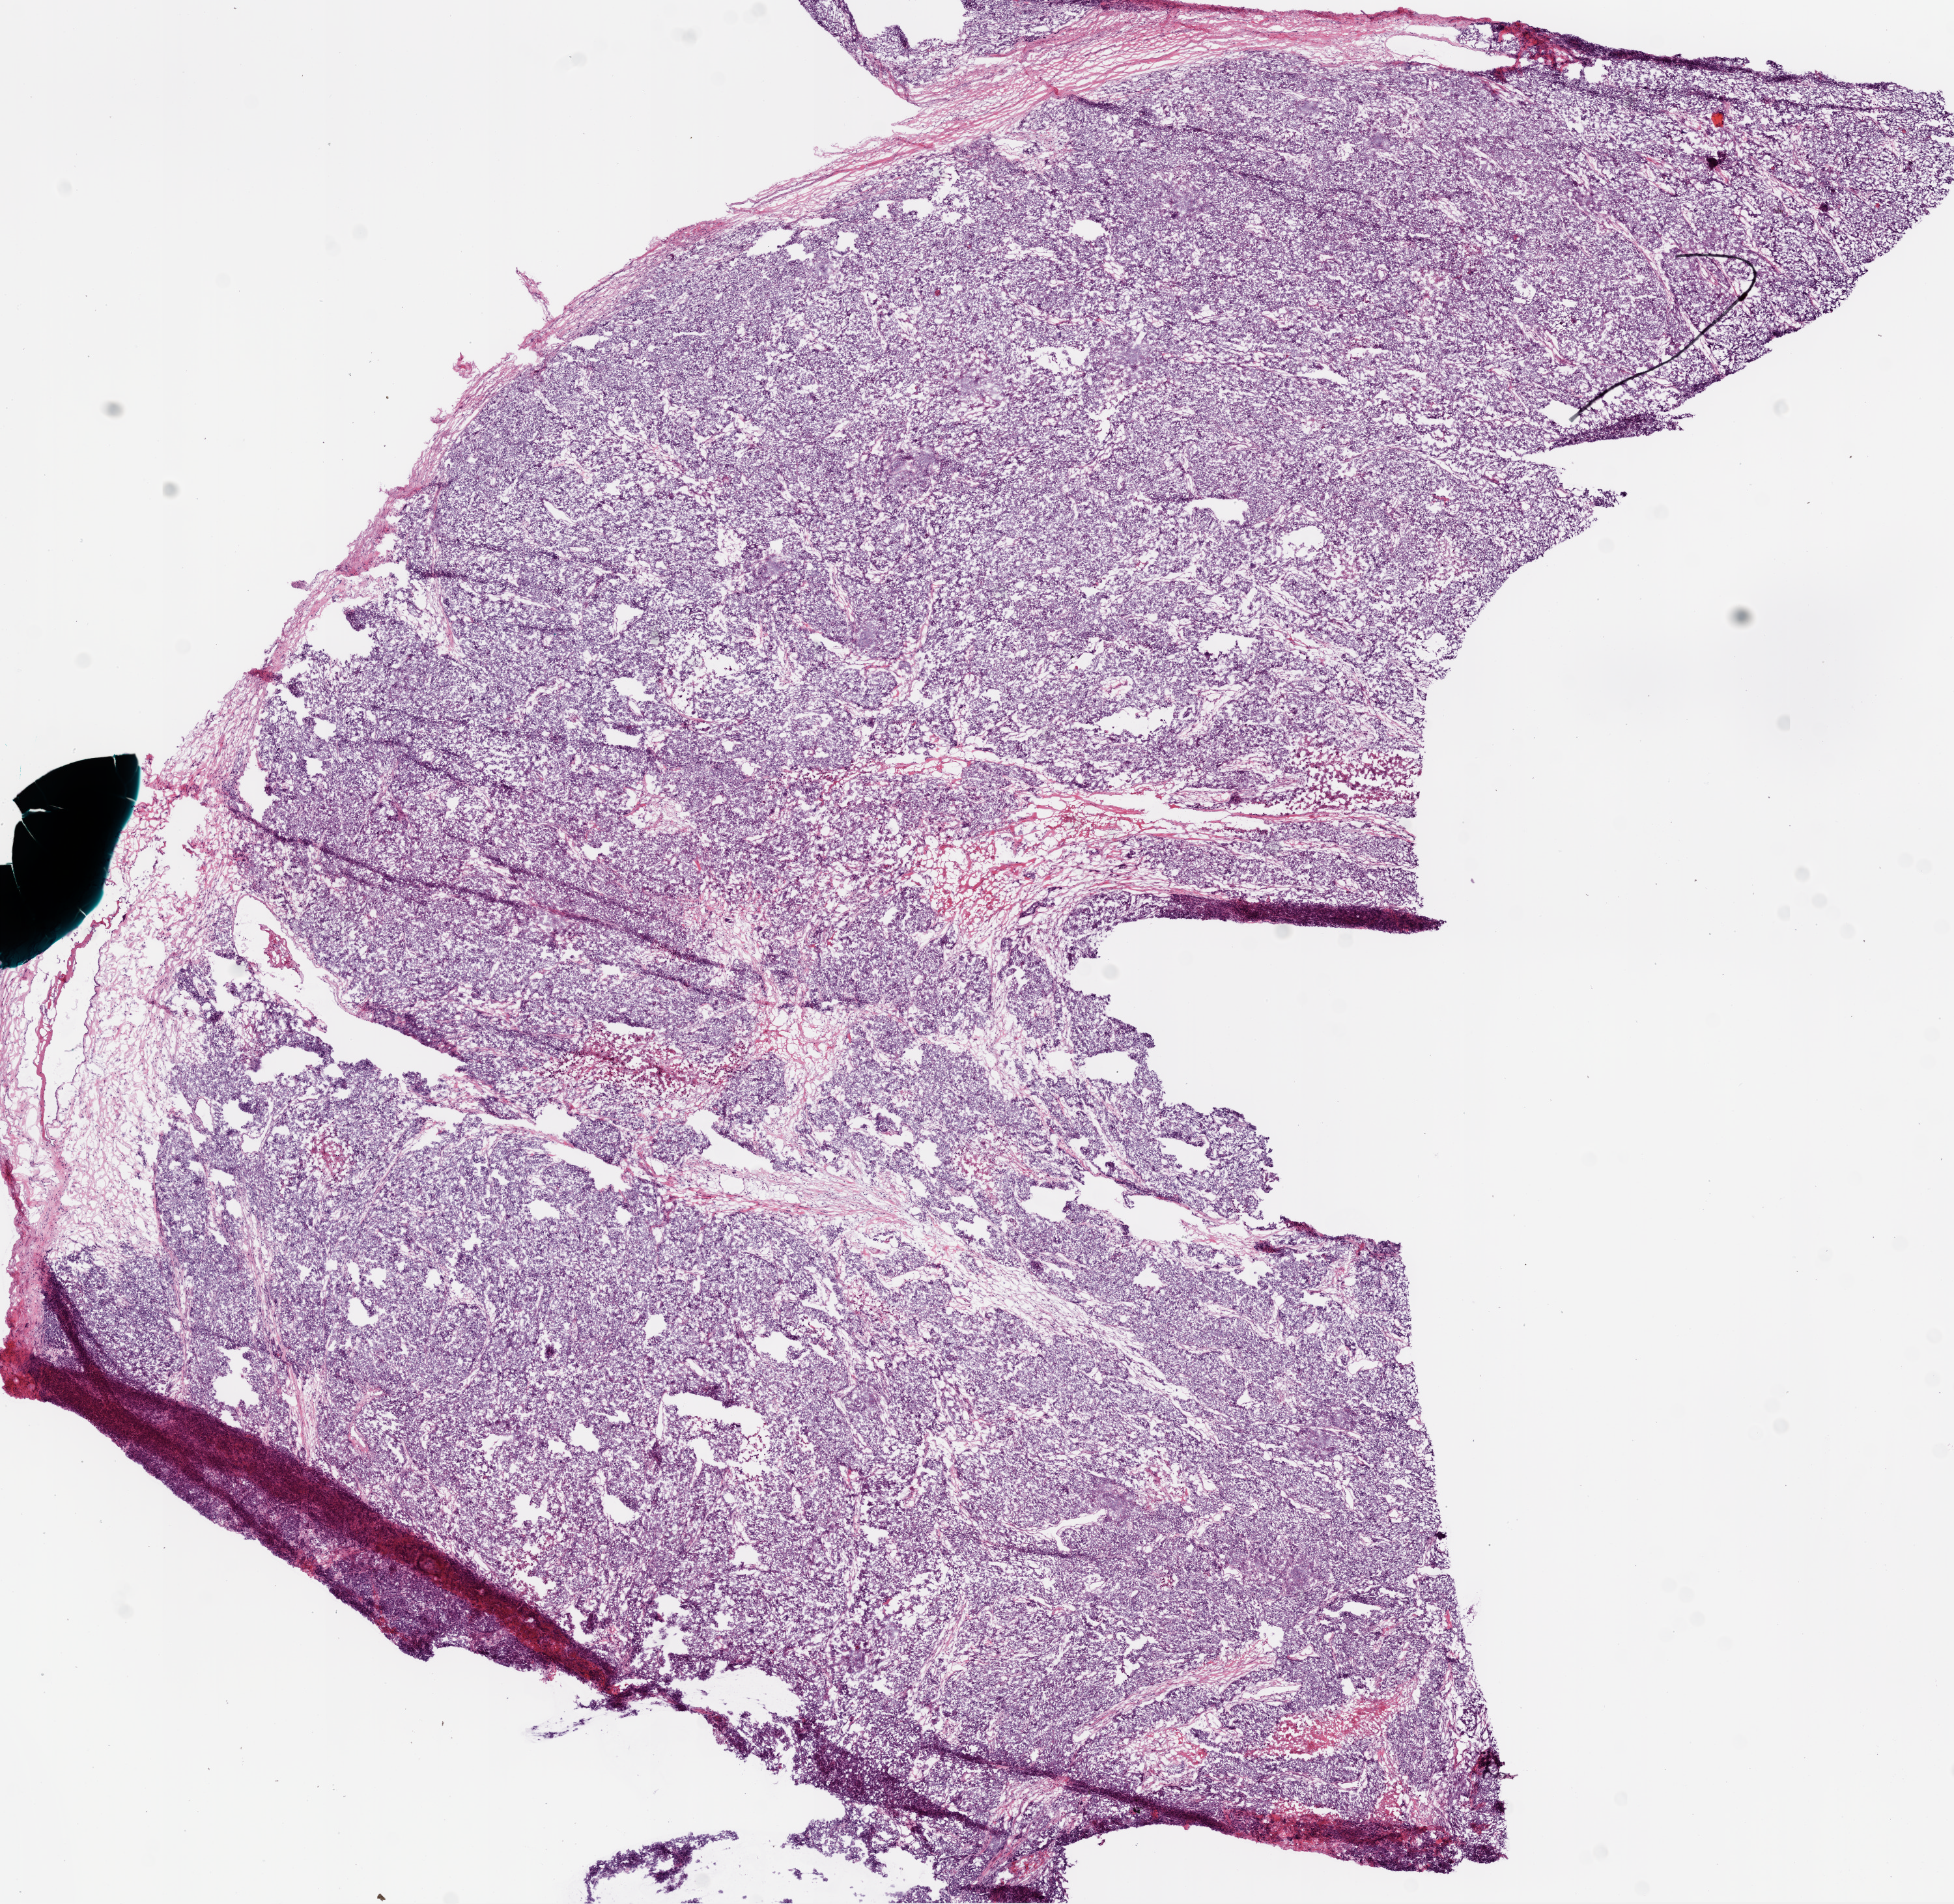
Whole-slide histology image, H&E-stained, shown as a low-resolution overview of the whole scanned area (about 12.0 x 11.7 mm); frozen section from the bottom of the tissue portion; primary tumour sample from the ovary. Female patient; age at initial diagnosis 50 years. Histologic grade: G3 (poorly differentiated). Slide review estimates, as recorded: tumour cells 85%, tumour nuclei 90%, normal cells 0%, stromal cells 10%, necrosis 5%.
• histologic diagnosis: Serous cystadenocarcinoma, NOS
• FIGO stage: IIIC